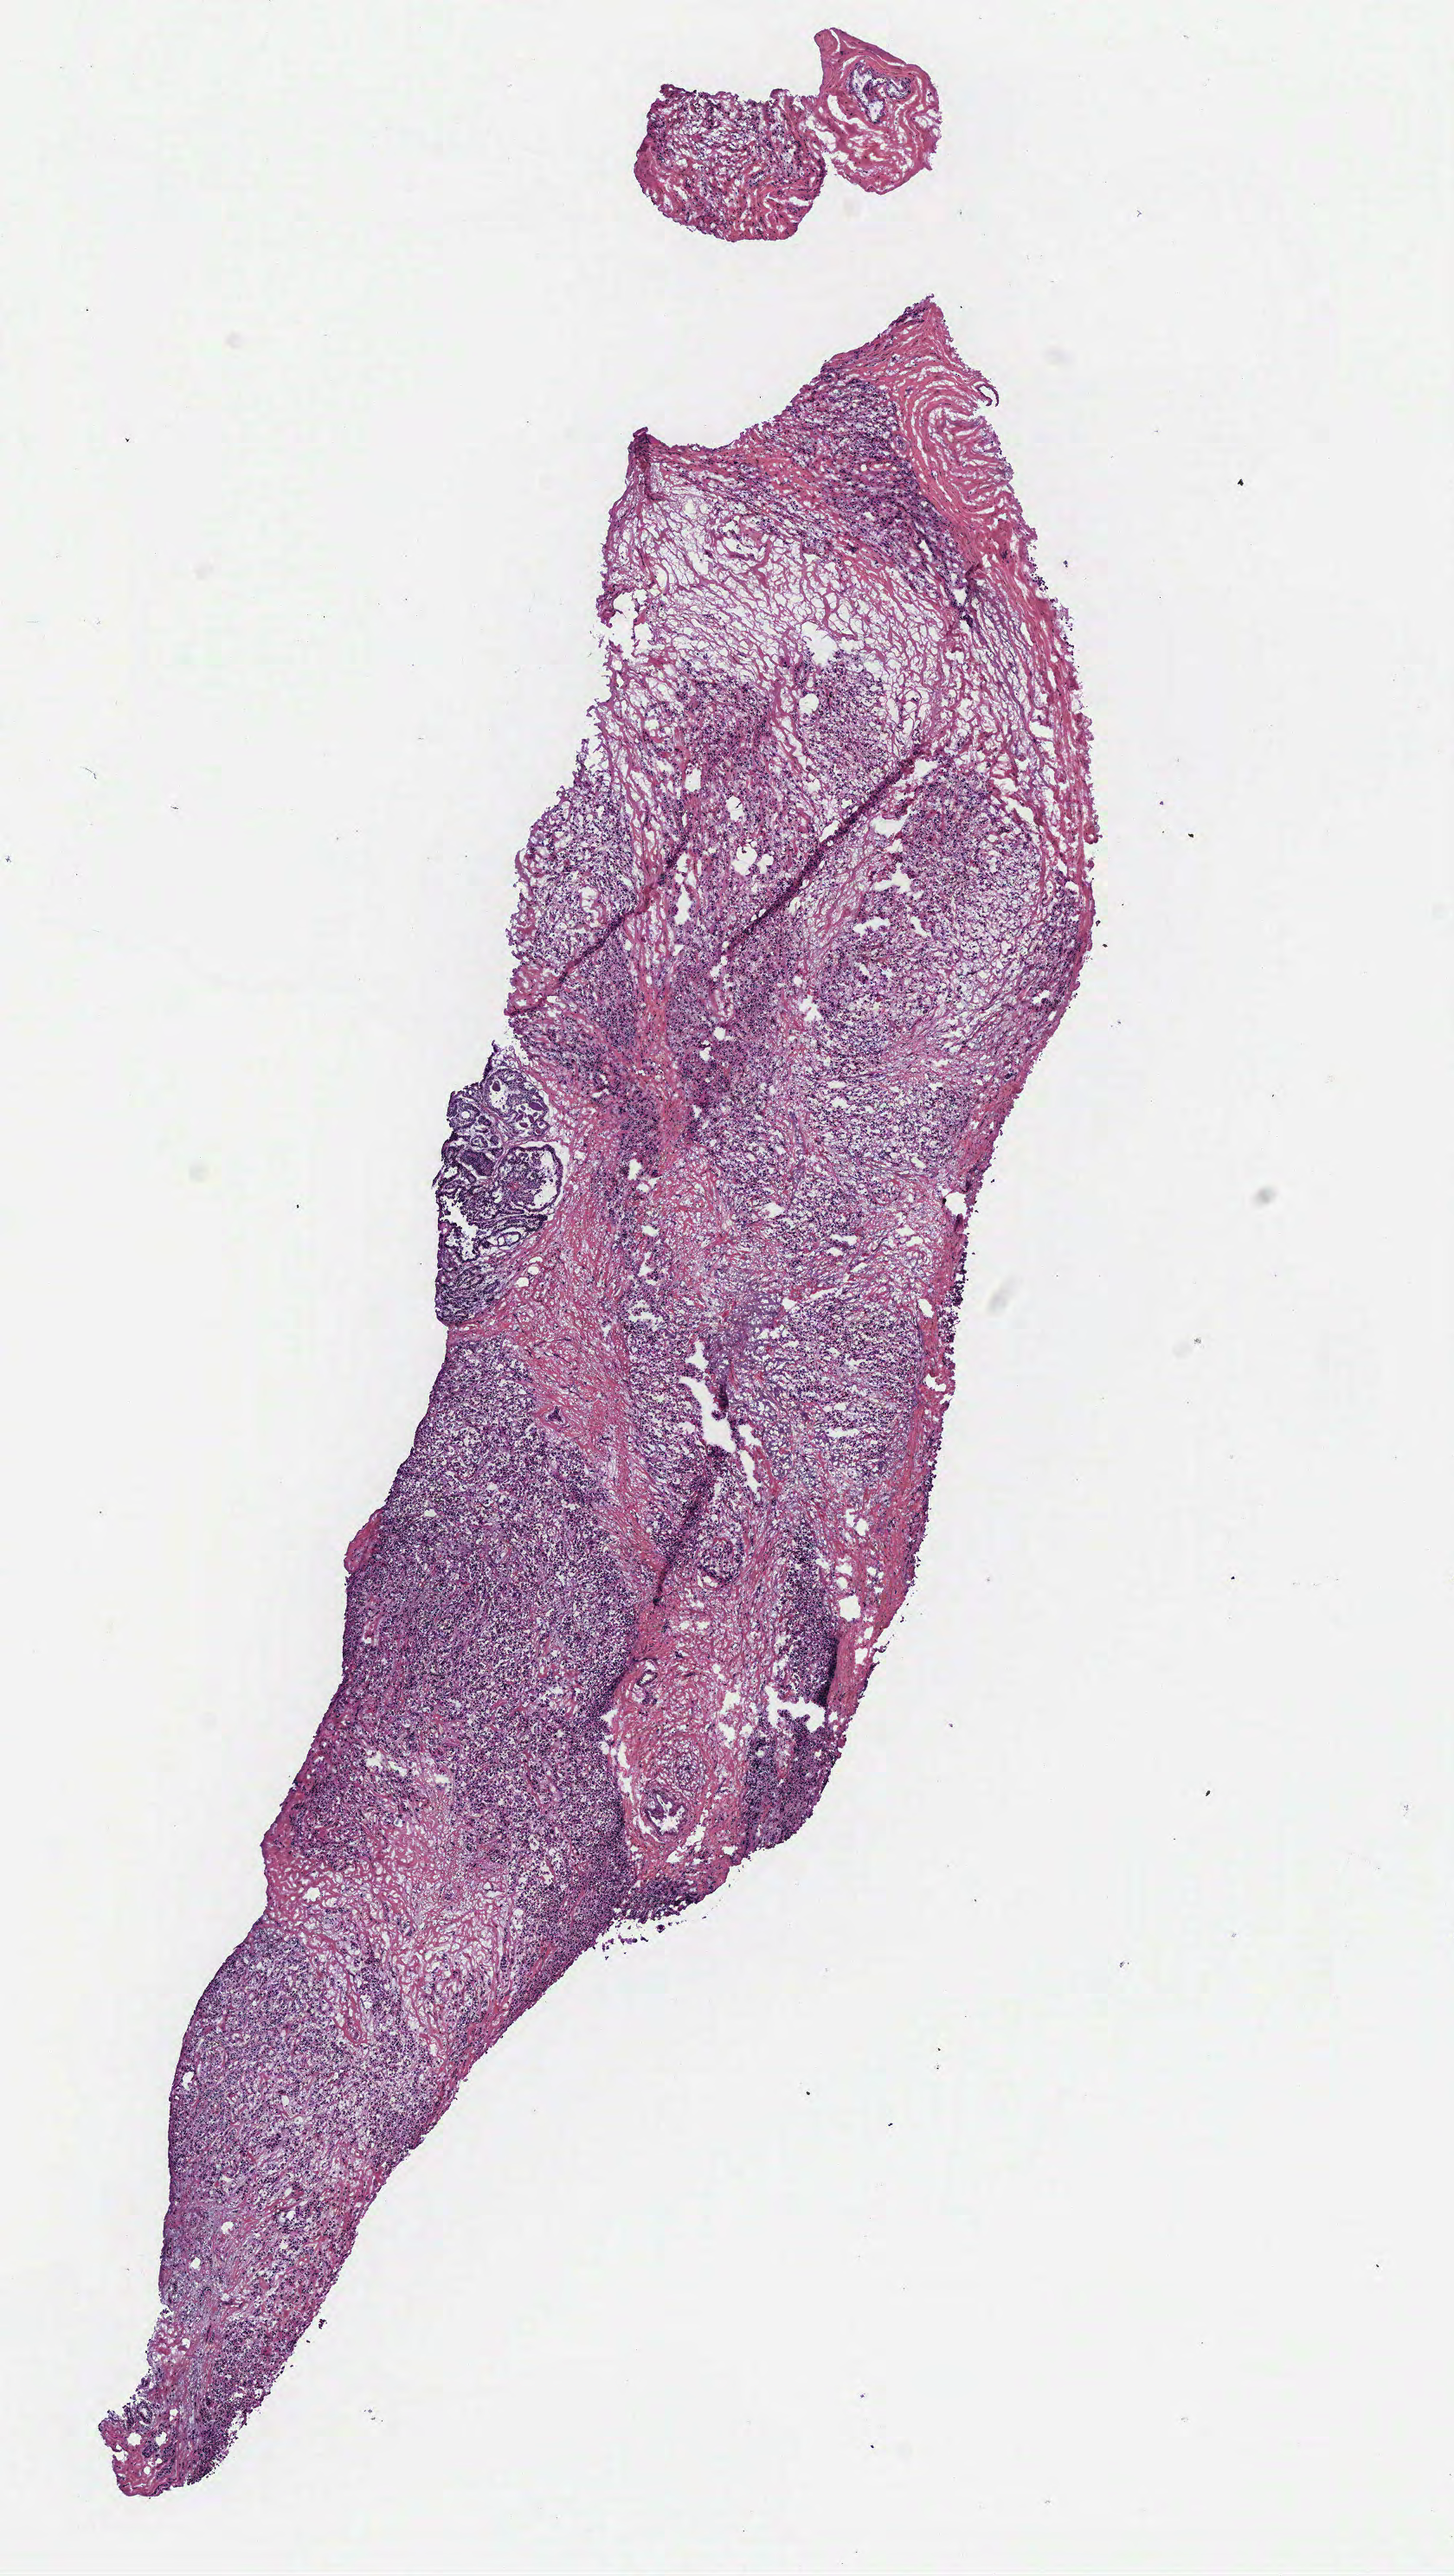
Whole-slide histology image, Hematoxylin and eosin (H&E) stained — shown as a low-resolution overview of the whole scanned area (about 6.7 x 11.9 mm, slide scanned at 40x). Tumour tissue sample, breast. Patient: female, age 78 years.
Histologic diagnosis: Infiltrating lobular carcinoma, NOS.